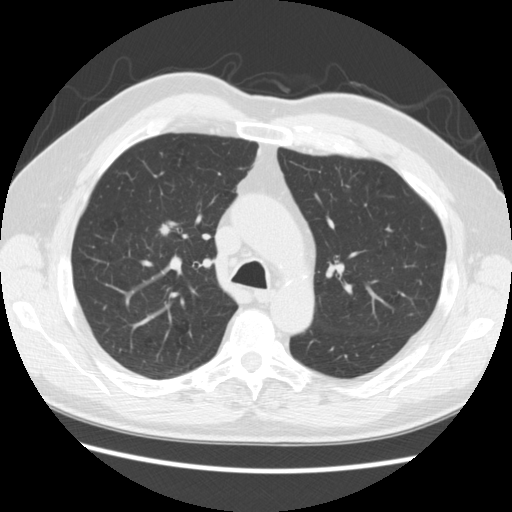
Chest CT (low-dose screening protocol), one axial image. Baseline screening round. Lung window (W 1500 / L -600 HU). 2.5 mm slice thickness. Standard (soft-tissue) reconstruction kernel (STANDARD). 512 × 512 image matrix. Male, age 69 years at enrolment.
Expert reader's lesion annotation, box from (x=151, y=215) to (x=191, y=245) px. Reader record for this screening exam (exam-level; its link to the box is not recorded): non-calcified nodule or mass ≥4 mm, right upper lobe, 9 × 7 mm, poorly defined margins, soft tissue attenuation. Official screen result: positive, change unspecified: nodule(s) >= 4 mm or enlarging nodule(s), mass(es), or other non-specific abnormalities suspicious for lung cancer. Lung cancer was diagnosed 50 days after this screen: adenocarcinoma, NOS, right upper lobe, moderately differentiated (G2), stage IA (AJCC 6th edition), 9 mm at pathology.